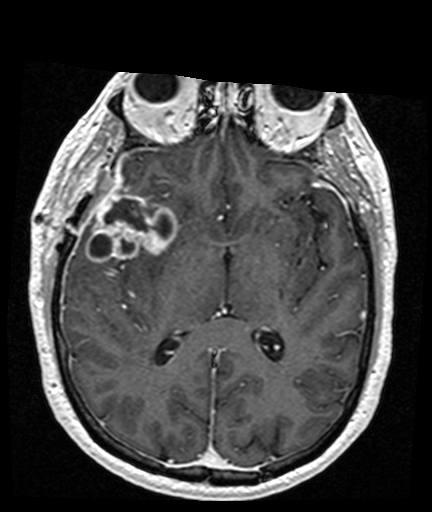
Brain MRI from a brain-tumour surgery series, one axial slice; position 85 of 176 along the scan axis; T1-weighted post-contrast; 432 × 512 image matrix, field of view 194 × 230 mm. Case-level facts recorded for this patient, not image findings: histopathology: Glioblastoma; WHO grade: 4; IDH mutation: no.
Annotated regions visible in this slice (outlined manually by an expert reader):
- tumour: bounding box <85,184,178,263> (left, top, right, bottom; pixels)